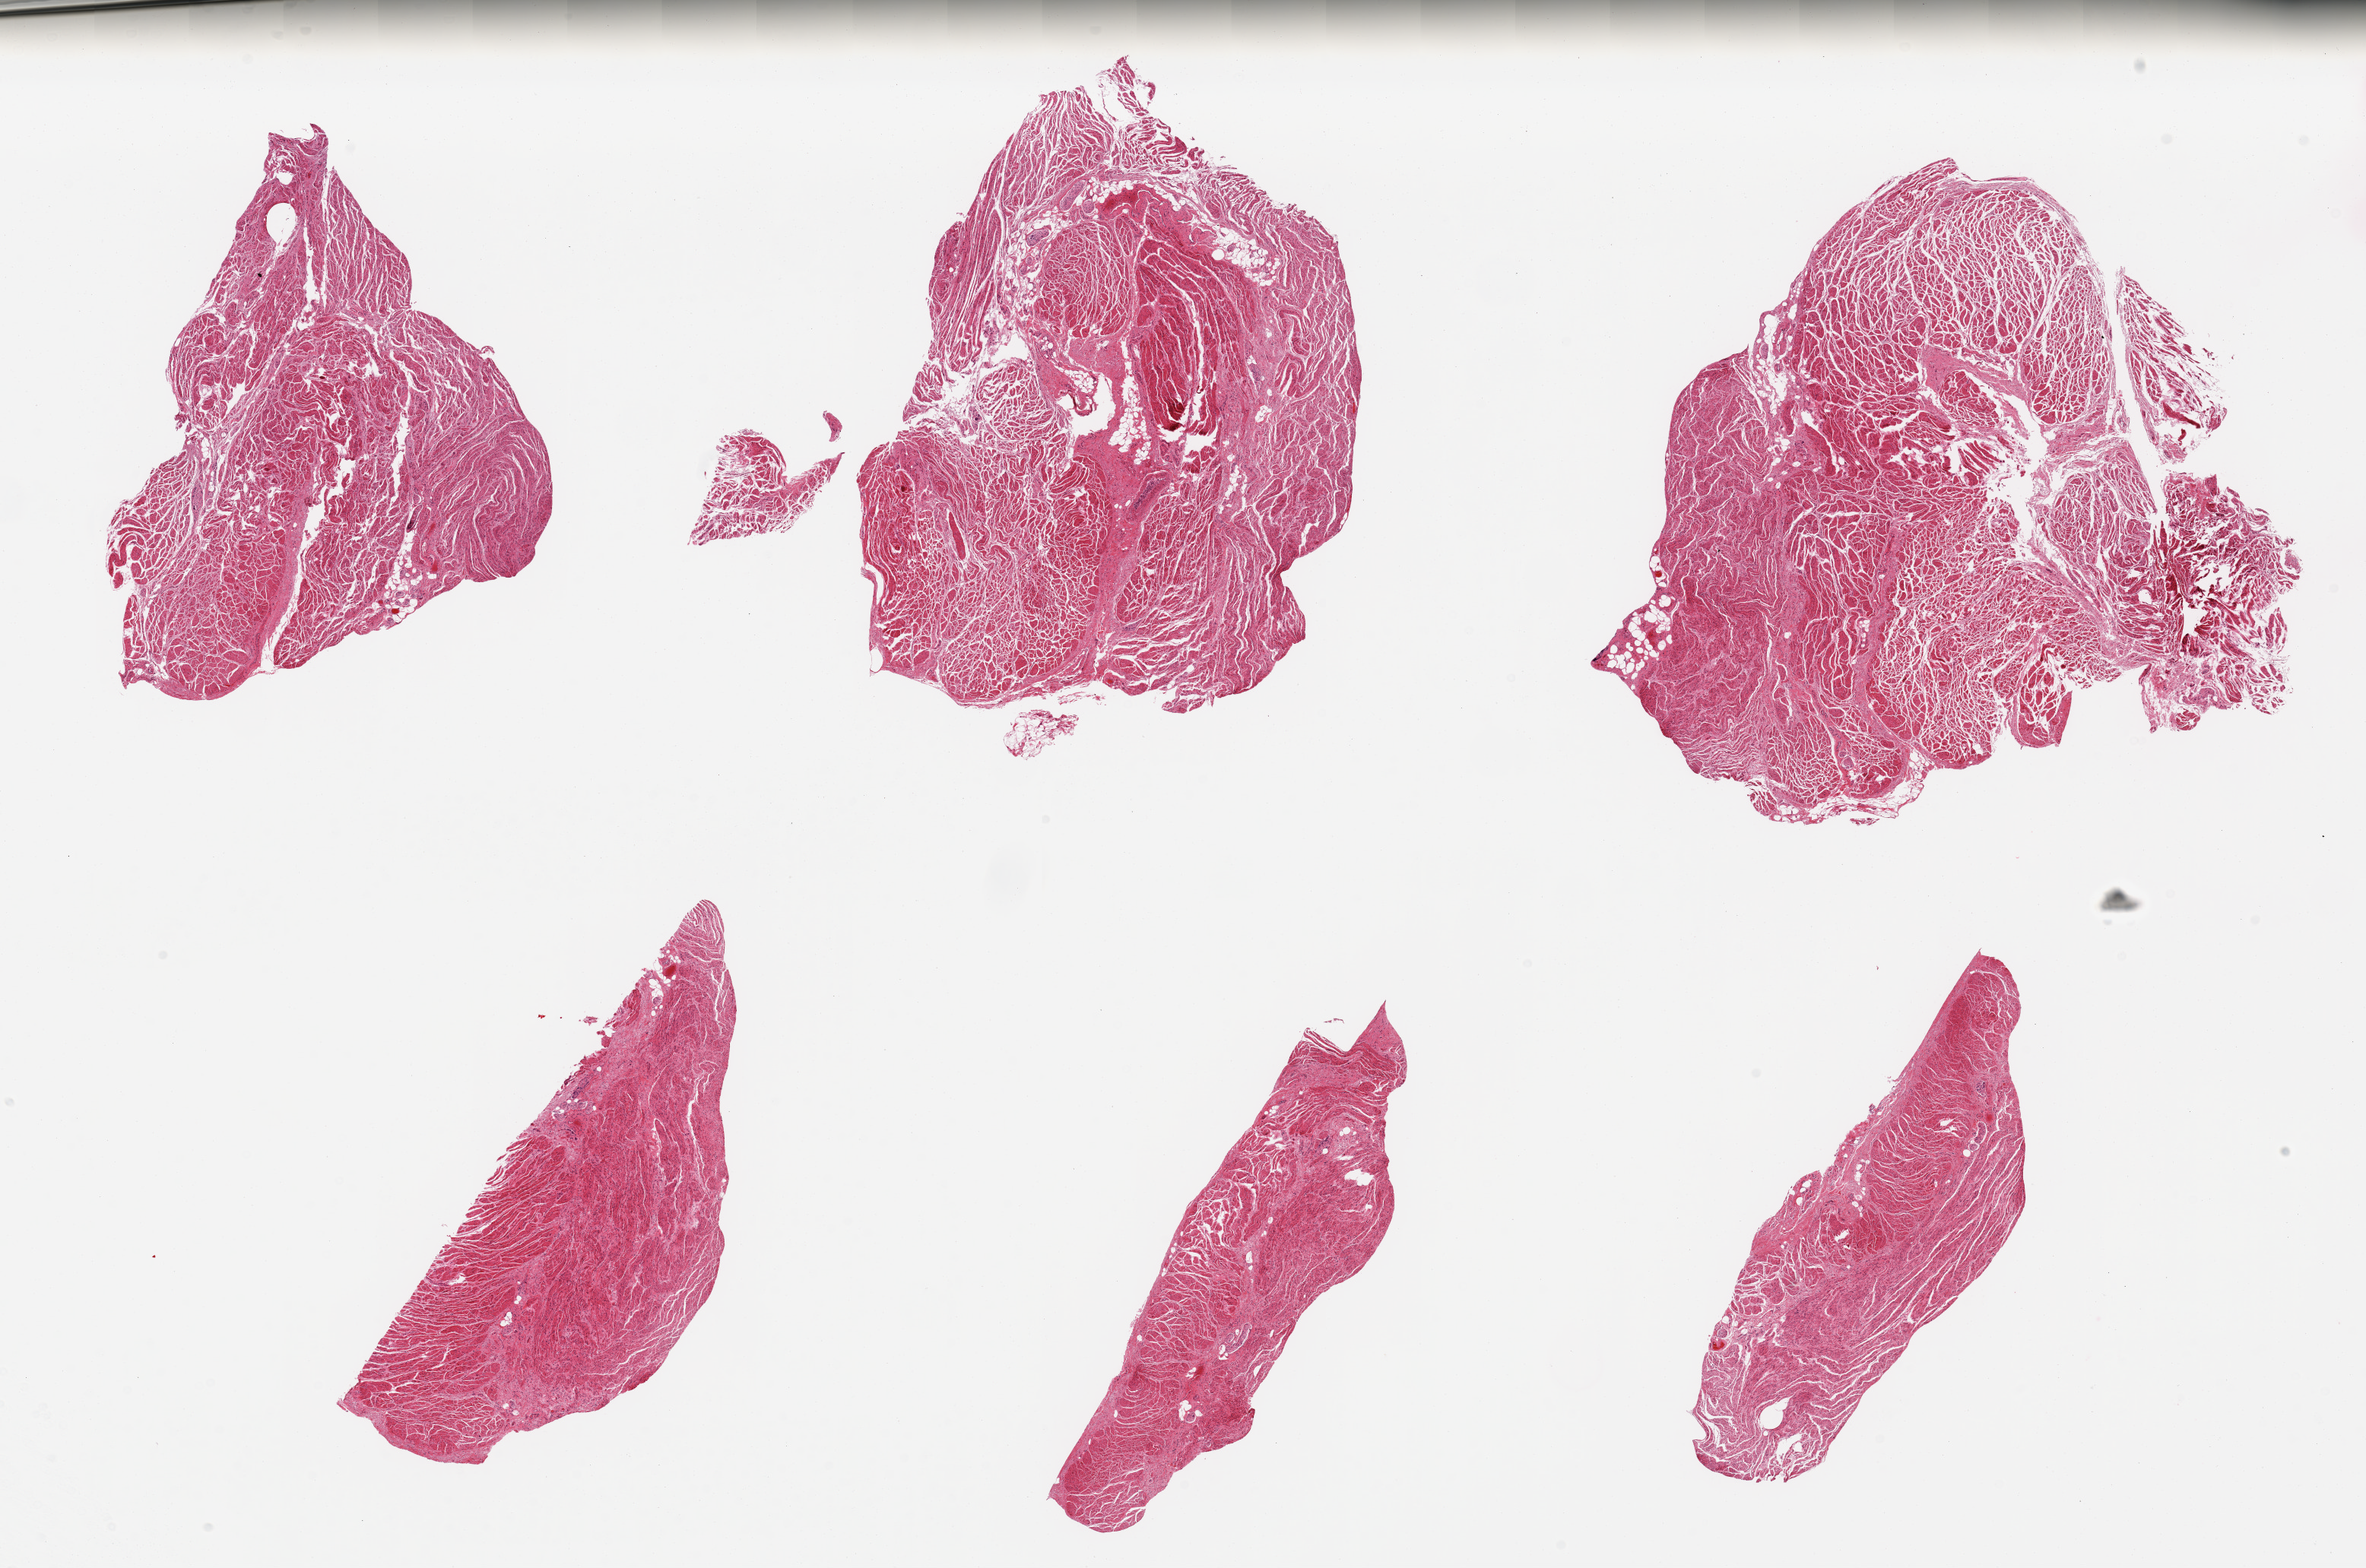
Digitized haematoxylin and eosin-stained section, brightfield, whole scanned area (about 24.6 x 16.3 mm, from a 20x scan) shown as a low-resolution overview. PAXgene-fixed paraffin-embedded (PFPE) section. Section of gastroesophageal junction (target tissue). Donor tissue sample. Donor: male.
Pathologist's review note for this sample: 6 pieces, all muscularis, good specimens.